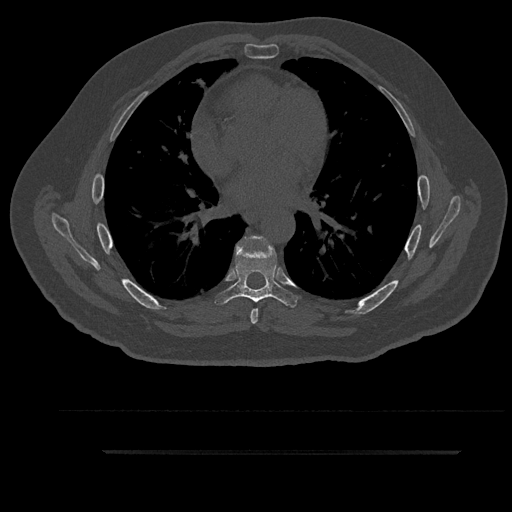
CT including the spine, one axial slice; position 540 of 797 along the scan axis; reconstruction kernel Br40s/3; bone window (W 1800 / L 400 HU); 0.5 mm slice thickness; 512 × 512 image matrix. Patient: male, 63 years. Case-level facts recorded for this patient, not image findings: primary cancer: renal; vertebrae with lytic lesions (as recorded): T8.
Annotated regions visible in this slice (semi-automatically segmented with operator editing):
- T6 vertebra: bounding box <248,236,264,324> (left, top, right, bottom; pixels)
- T7 vertebra: <215,238,298,307>